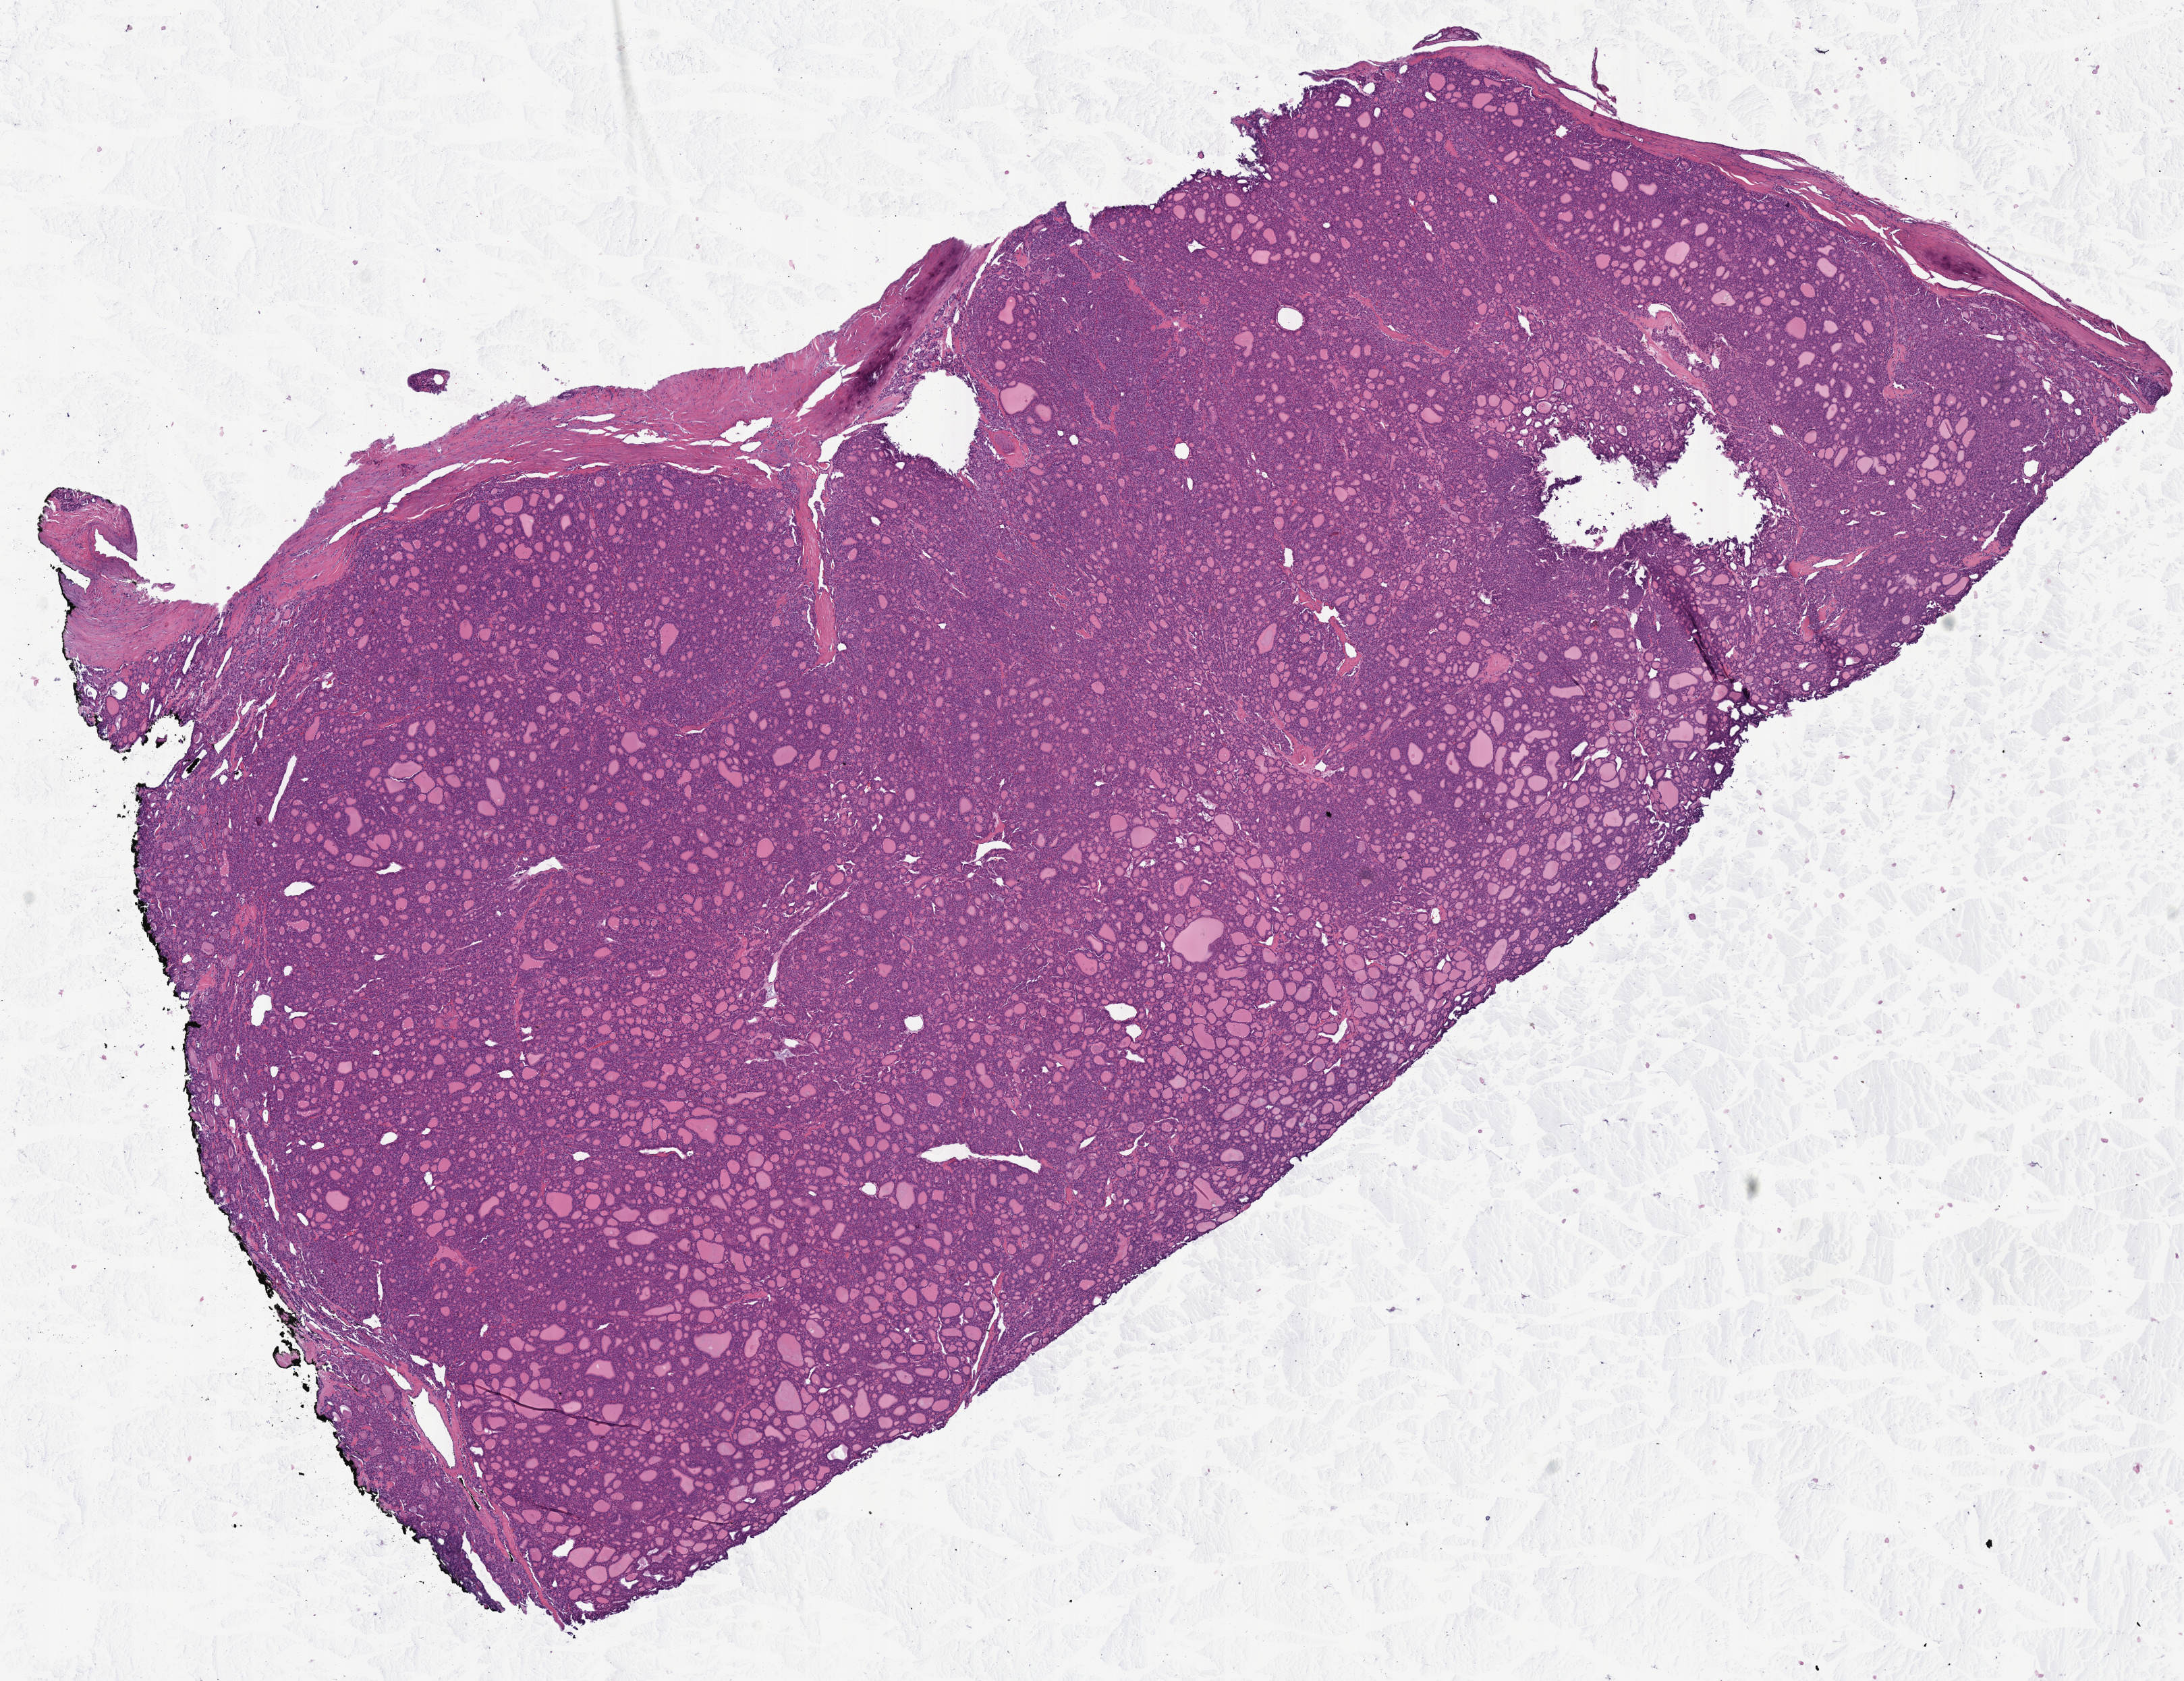
Whole-slide histology image, H&E-stained — a low-resolution overview of the entire scanned area, about 12.7 x 9.8 mm (slide scanned at 40x), formalin-fixed paraffin-embedded (FFPE) diagnostic section, sample: primary tumour, thyroid. Male, age 69 years at initial diagnosis.
Histologic diagnosis: Papillary carcinoma, follicular variant (thyroid gland).